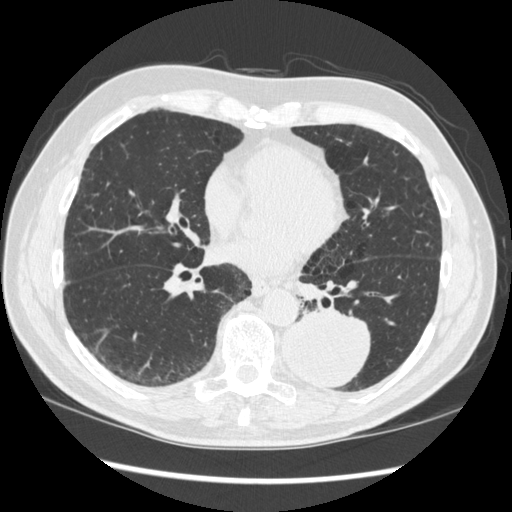
Low-dose screening chest CT, one axial slice; position 142 of 348 along the scan axis; reconstruction kernel STANDARD; lung window (W 1500 / L -600 HU); 1.25 mm slice thickness; 512 × 512 image matrix.
Annotated regions visible in this slice (outlined manually by an expert reader):
- lesion 1 (tumor, lower lobe of left lung): bounding box <283,310,371,389> (left, top, right, bottom; pixels)